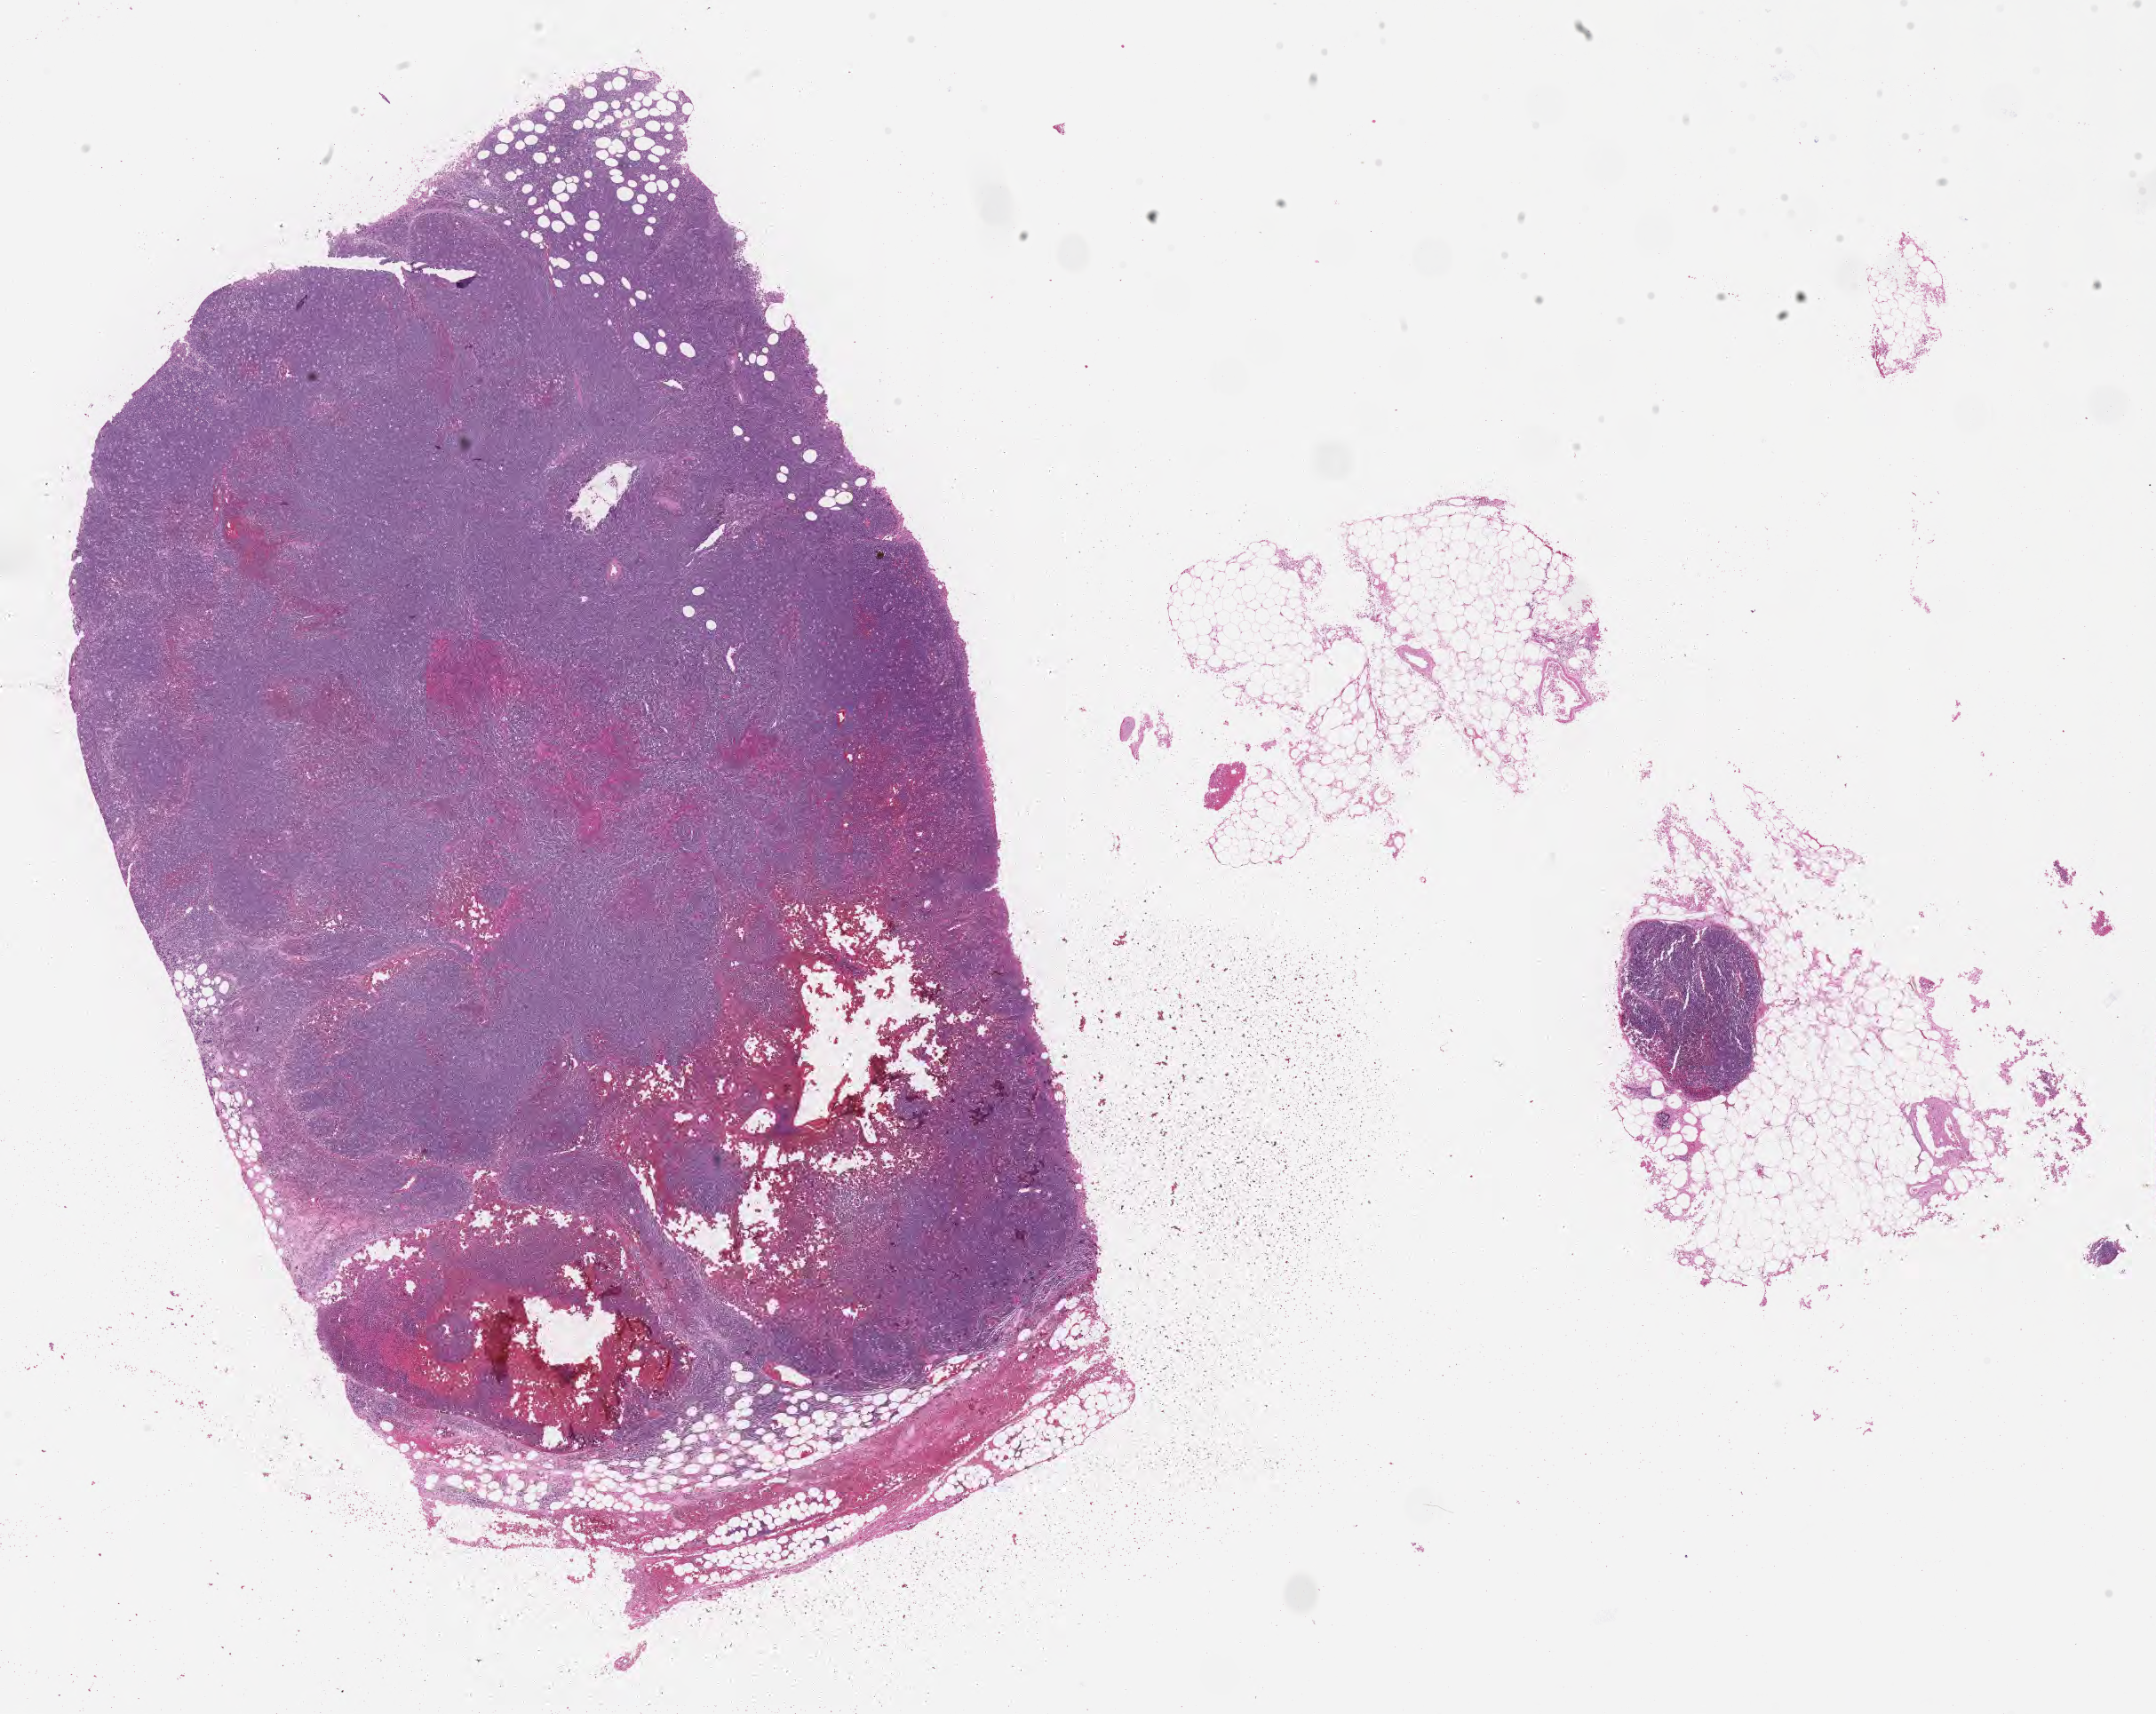
Whole-slide image, hematoxylin and eosin (H&E) stain — low-resolution overview of the scanned area, about 19.6 x 15.6 mm, formalin-fixed paraffin-embedded section, specimen: primary tumor. Patient male; 40 years old.
Histologic diagnosis: Burkitt lymphoma, NOS.